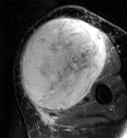
MRI of an extremity soft-tissue mass, one axial slice. T2-weighted fat-saturated. MR volume resampled by the dataset authors to the PET/CT grid (not the native acquisition matrix). 127 × 138 image matrix. Female patient. Case-level facts recorded for this patient, not image findings: histological type: pleiomorphic leiomyosarcoma; grade: high; site of the primary tumour: left biceps.
Structures marked on this image (expert contour drawn on MRI and transferred to this co-registered scan by the dataset authors):
- gross tumour volume including surrounding oedema: bounding box (x1, y1, x2, y2) in pixels: (20, 18, 108, 113)
- gross tumour volume (mass): (20, 18, 108, 111)